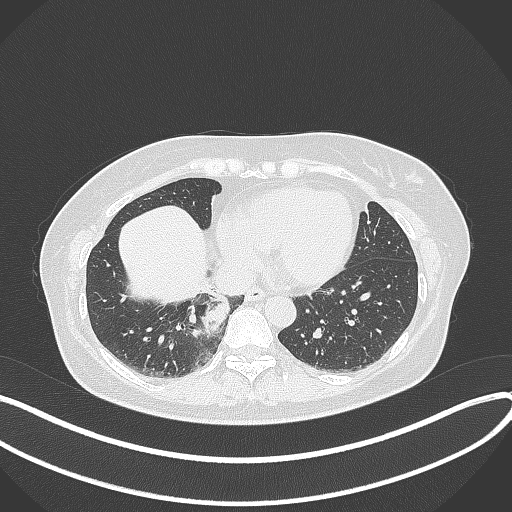
Chest CT, one axial slice. Slice 107 of 331 in the series (ordered by position). 120 kVp. Lung window (W 1500 / L -600 HU). 512 × 512 image matrix. Patient: female, 54 years. From the clinical record (not read from this slice): clinical TNM (as recorded): T4 N0 M0.
Annotated regions visible in this slice (bounding box drawn by a radiologist):
- lung tumour (recorded histology: adenocarcinoma): bounding box [x1, y1, x2, y2] px = [195, 289, 233, 330]